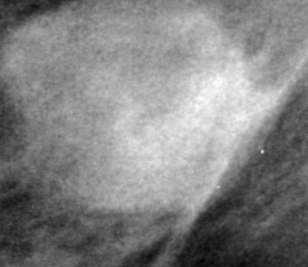
Crop from a digitized film mammogram around one marked abnormality, left breast, MLO view, BI-RADS breast density category 3 (scale 1–4).
Finding: mass, shape lobulated, margins obscured; BI-RADS assessment category 4; pathology result (as recorded, not read from the image): malignant.